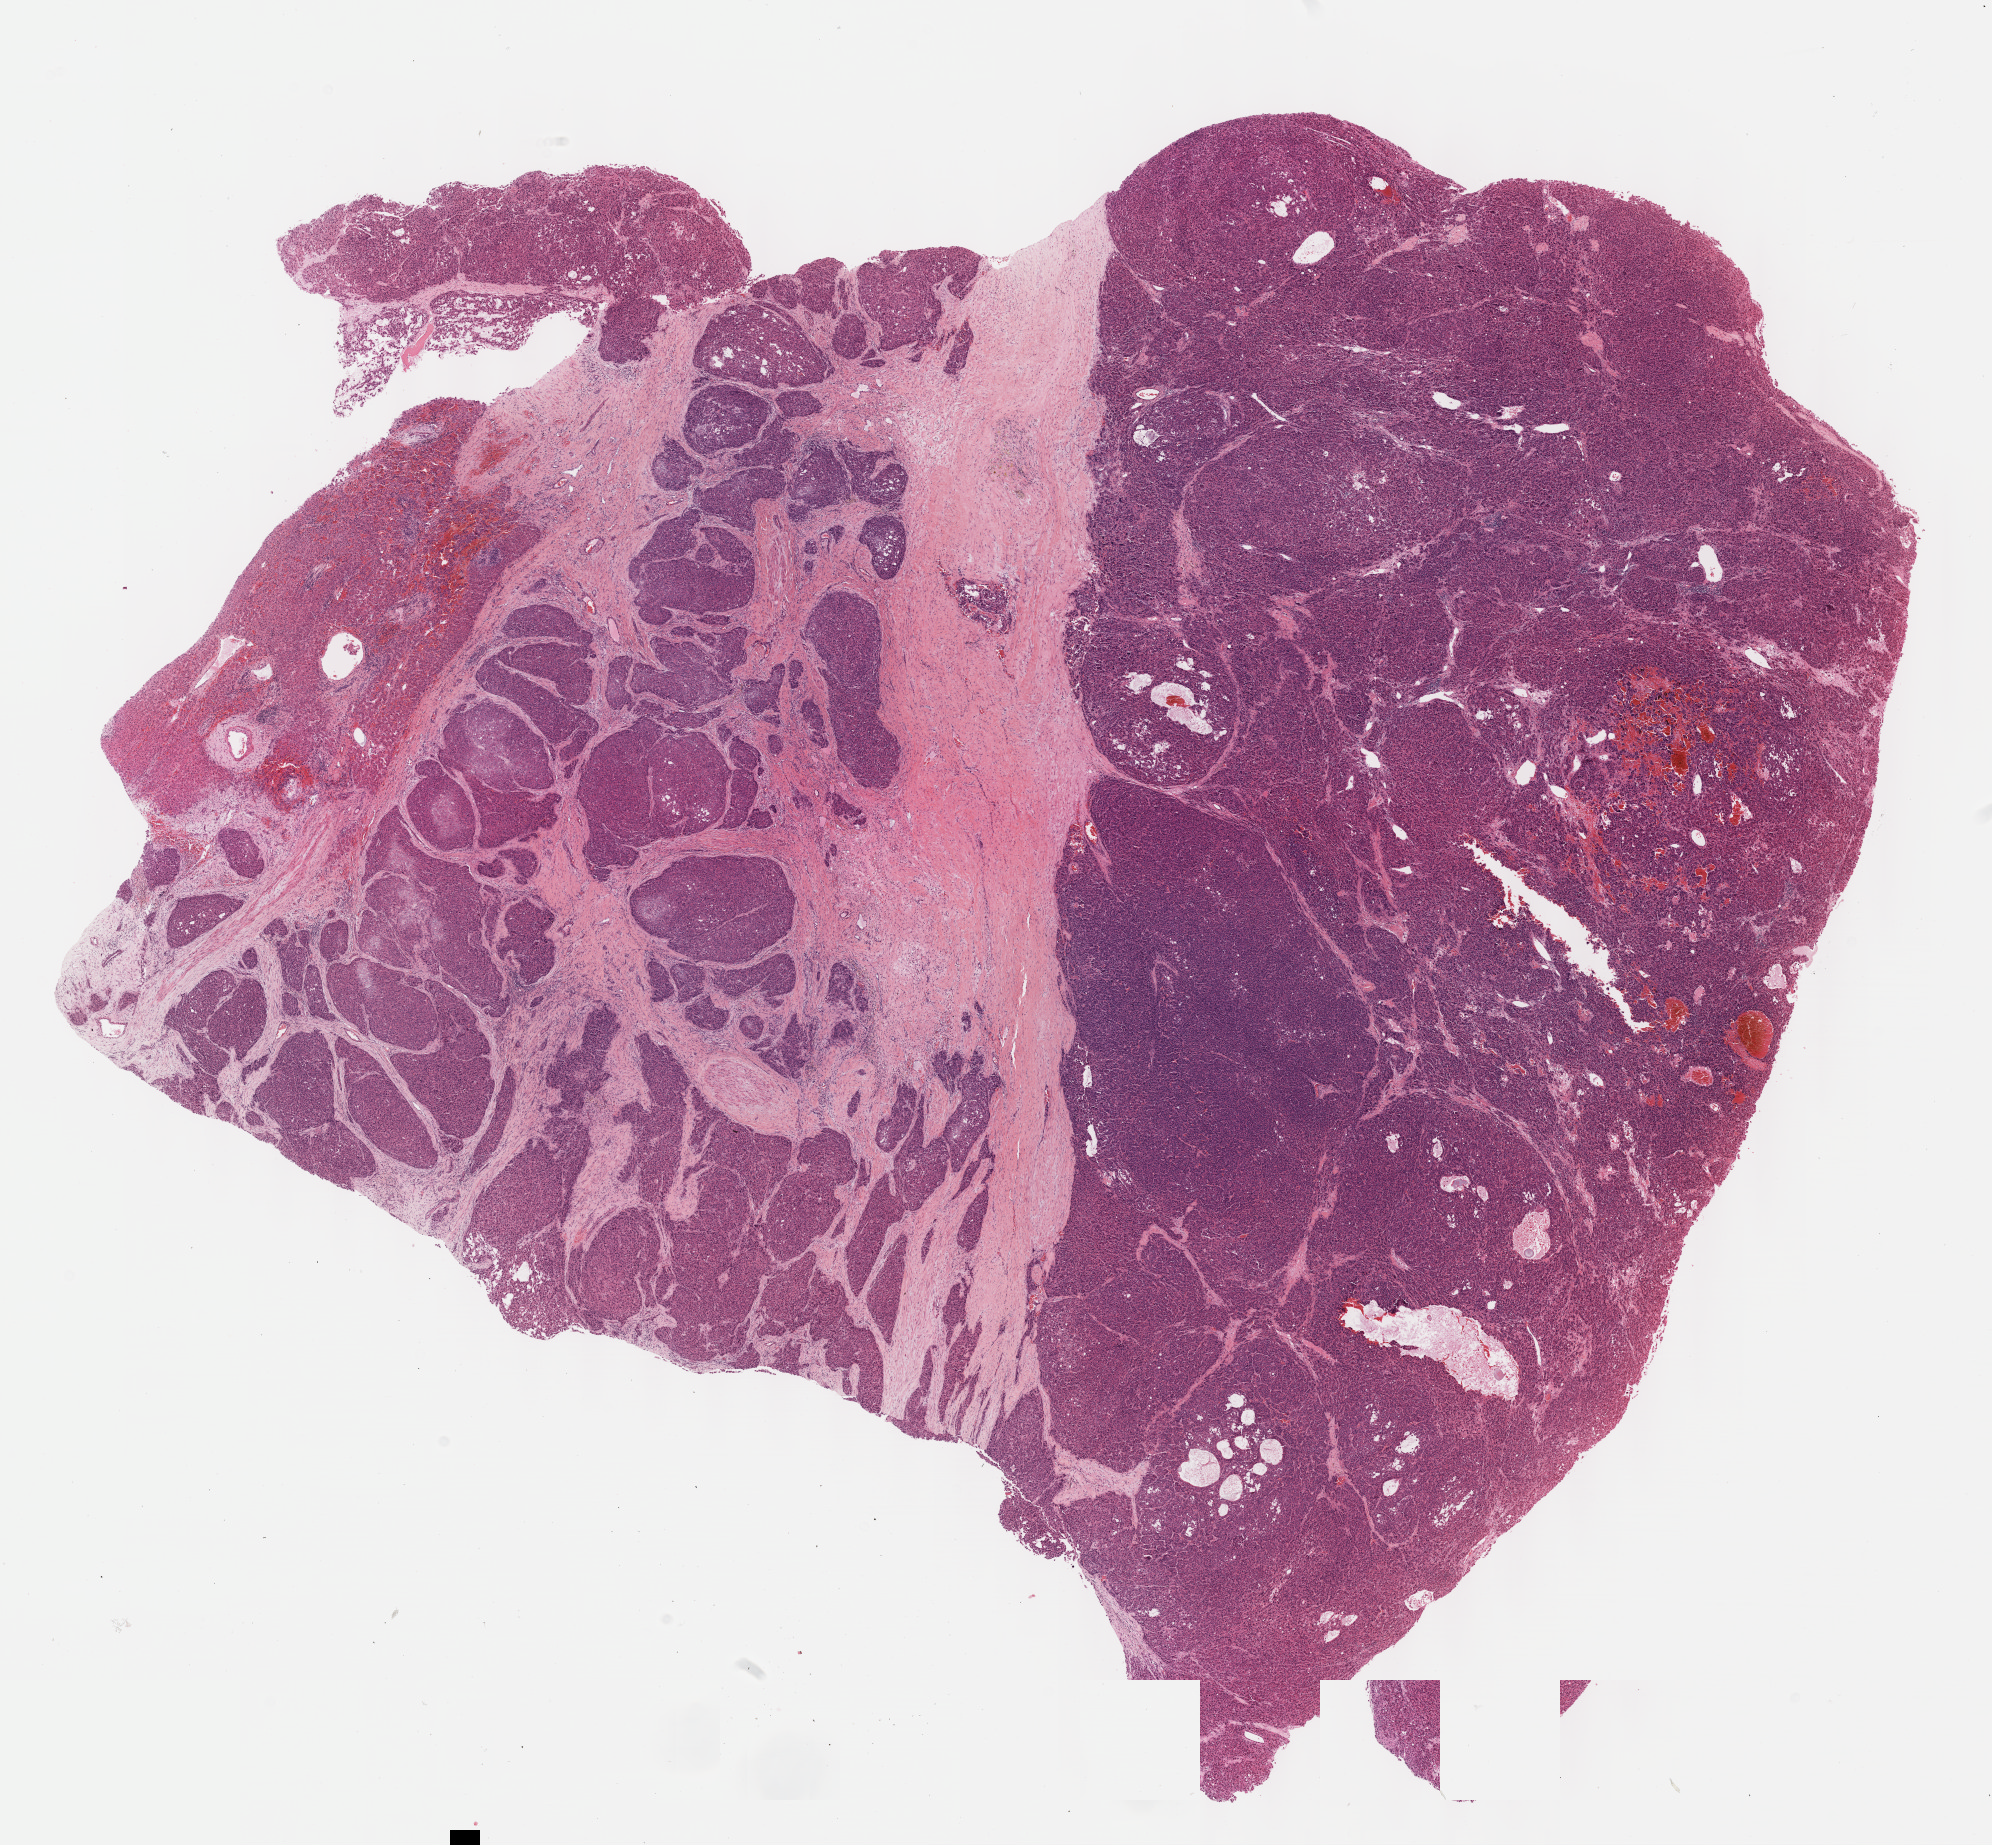
Whole-slide histology image, H&E-stained — whole scanned area (about 16.1 x 14.9 mm, slide scanned at 40x) shown as a low-resolution overview; formalin-fixed paraffin-embedded (FFPE) diagnostic section; liver, primary tumour sample. Patient: male, age at initial diagnosis 58 years. Histologic grade: G2 (moderately differentiated).
AJCC pathologic stage: II (7th edition). Histologic diagnosis: Hepatocellular carcinoma, NOS.